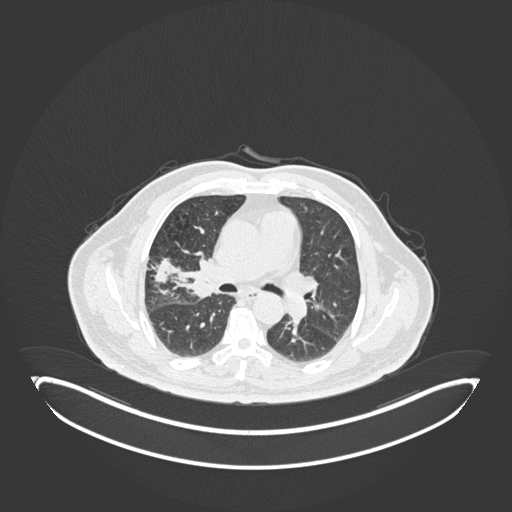
Chest CT, one axial slice; position 100 of 247 along the scan axis; 120 kVp; lung window (W 1500 / L -600 HU); 1 mm slice thickness; 512 × 512 image matrix, field of view 500 × 500 mm. Patient: male, 72 years. From the clinical record (not read from this slice): clinical TNM (as recorded): T1c N0 M0; histopathological grade: G2.
Structures marked on this image (rectangle marked by the reading radiologist):
- lung tumour (recorded histology: squamous cell carcinoma): bounding box <182,247,212,297> (left, top, right, bottom; pixels)